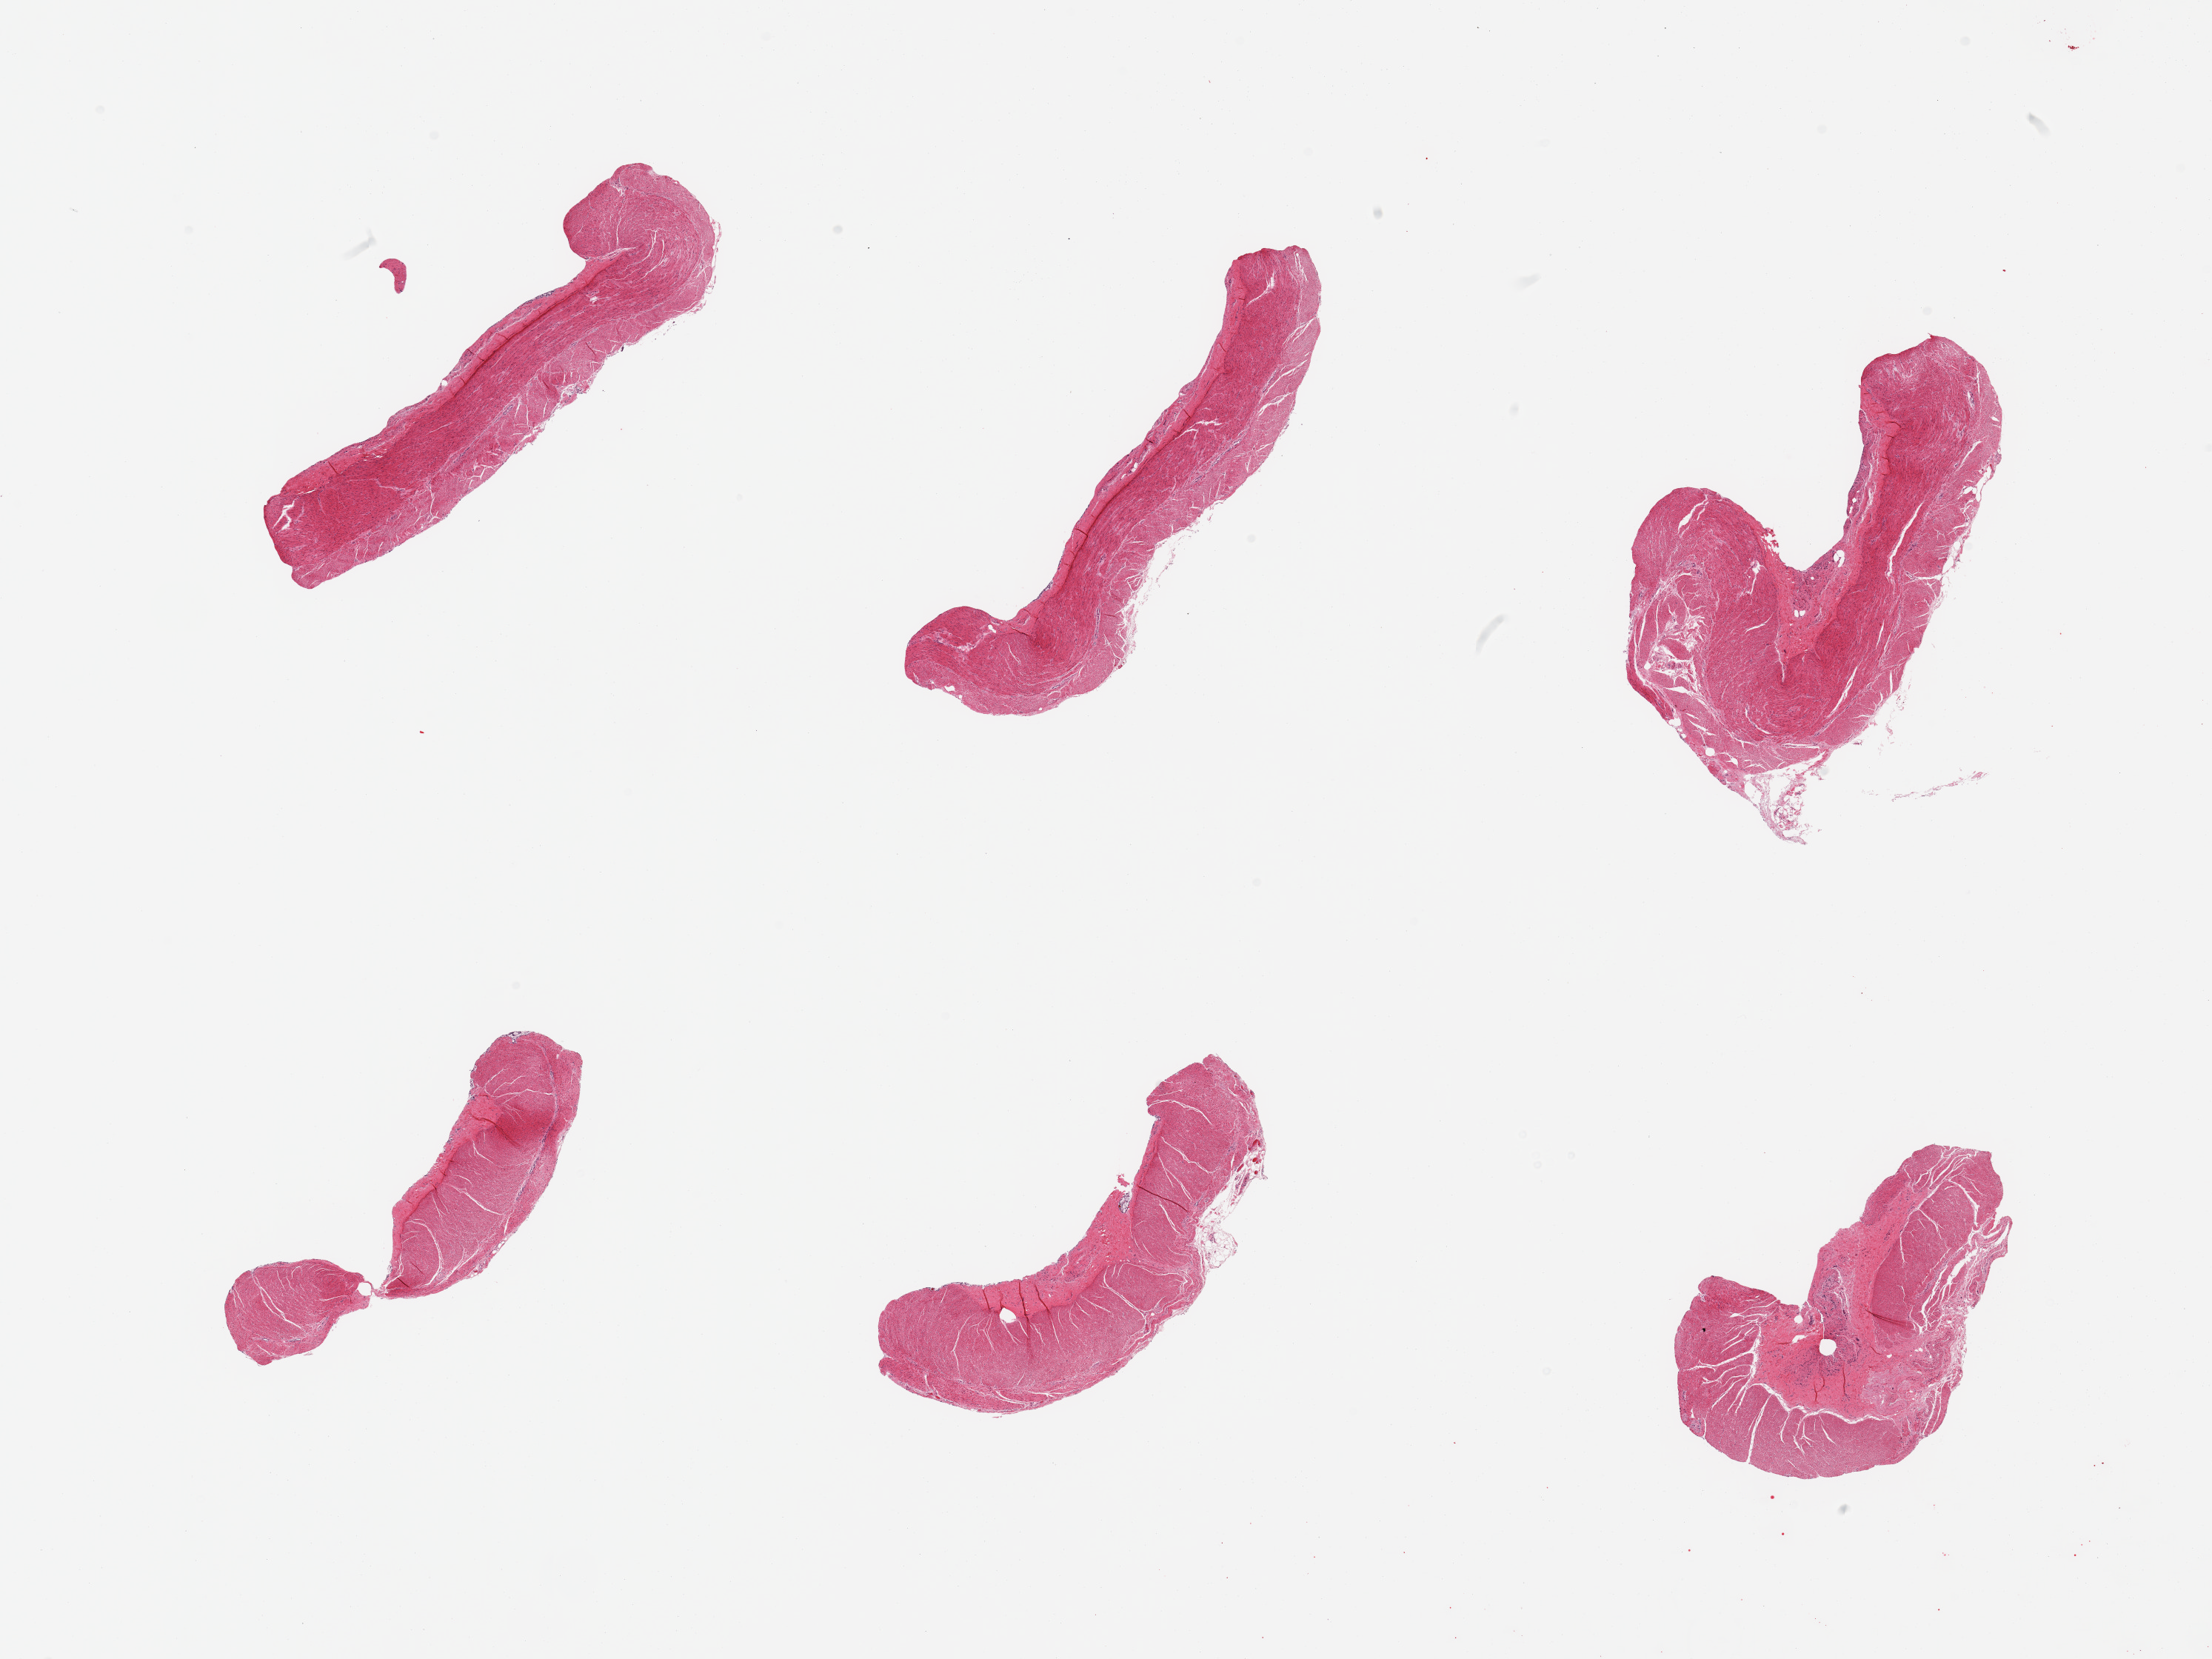
H&E whole-slide image, low-resolution overview of the scanned area, about 23.6 x 17.7 mm (acquisition: 20x scan), PAXgene-fixed, paraffin-embedded tissue, section of sigmoid colon (target tissue), tissue donor sample. Donor sex: male.
* reviewer comment on this tissue sample: 6 pieces; prominent submucosal fibrous stroma on 3 pieces, up to 40%